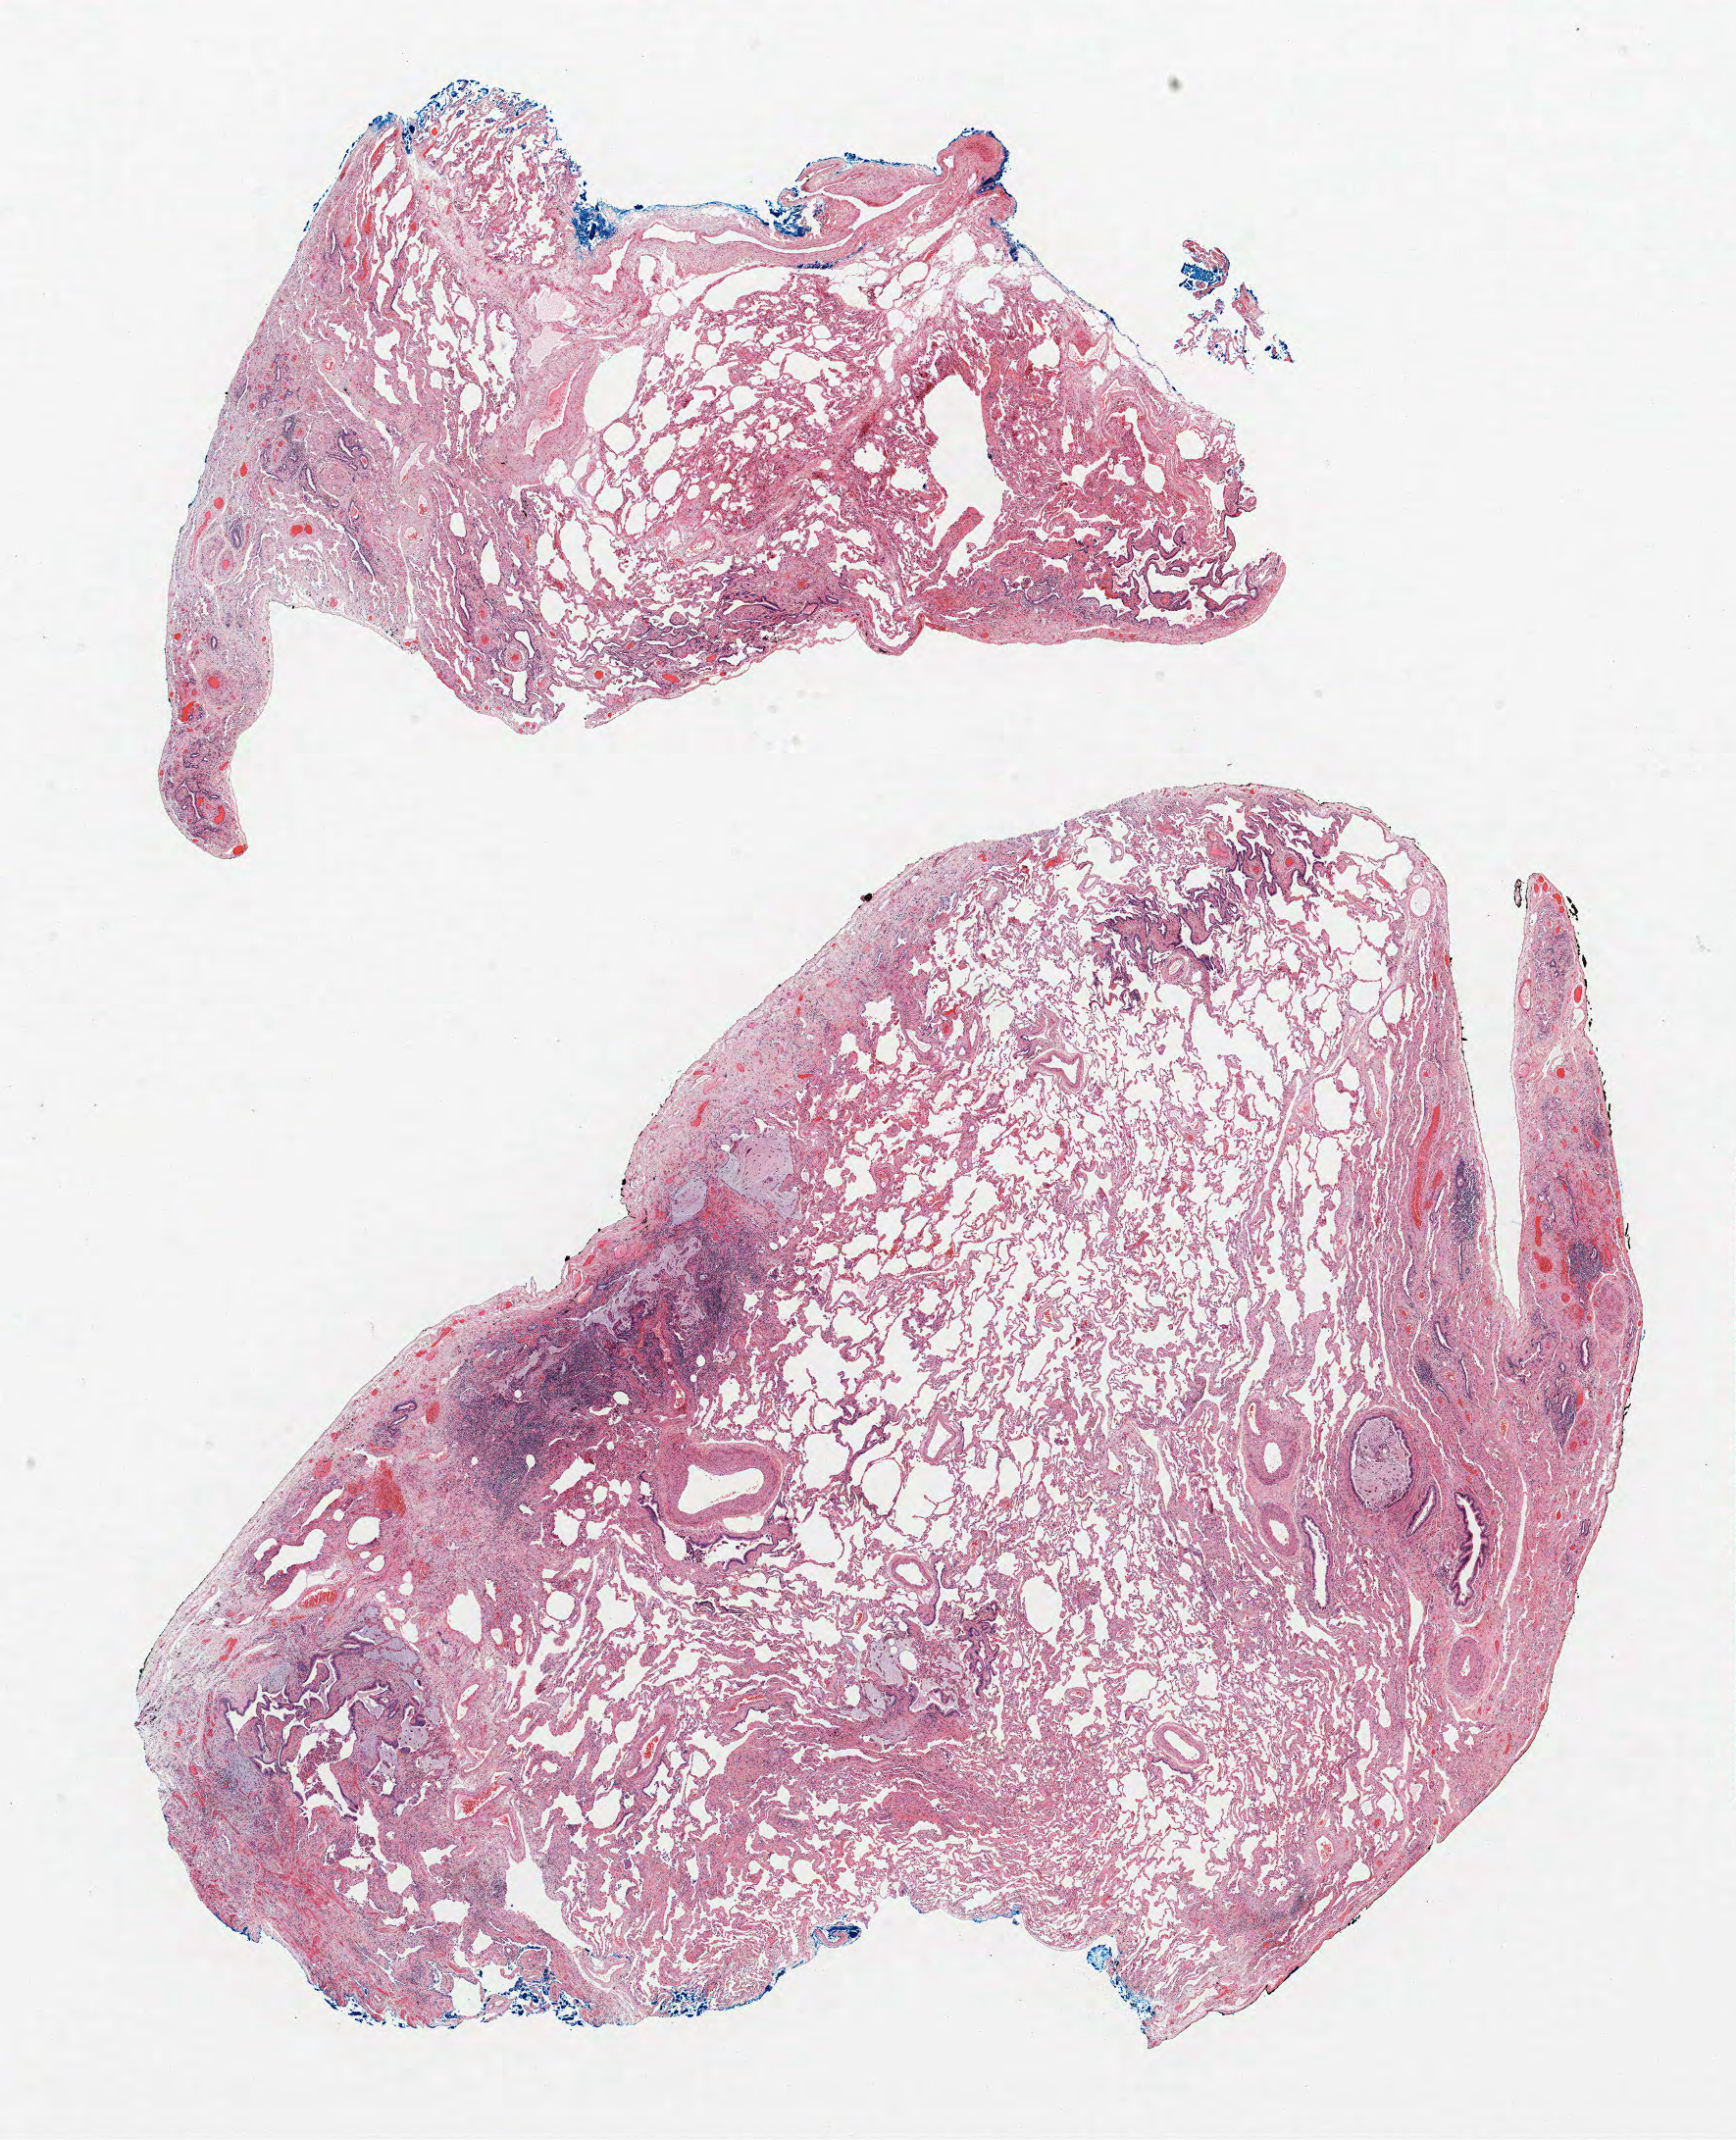
H&E-stained whole-slide image, low-resolution overview of the scanned area, about 14.2 x 17.5 mm (acquisition: 40x scan), formalin-fixed paraffin-embedded (FFPE) section, lung tissue. Male, age 66 at enrolment. Former smoker at enrolment. Grade: moderately differentiated (G2).
Stage (AJCC 6th edition): IIB. Participant's lung-cancer diagnosis: Adenocarcinoma, NOS. Tumour size (pathology): 9 mm. Primary tumour location (clinical record): left upper lobe.